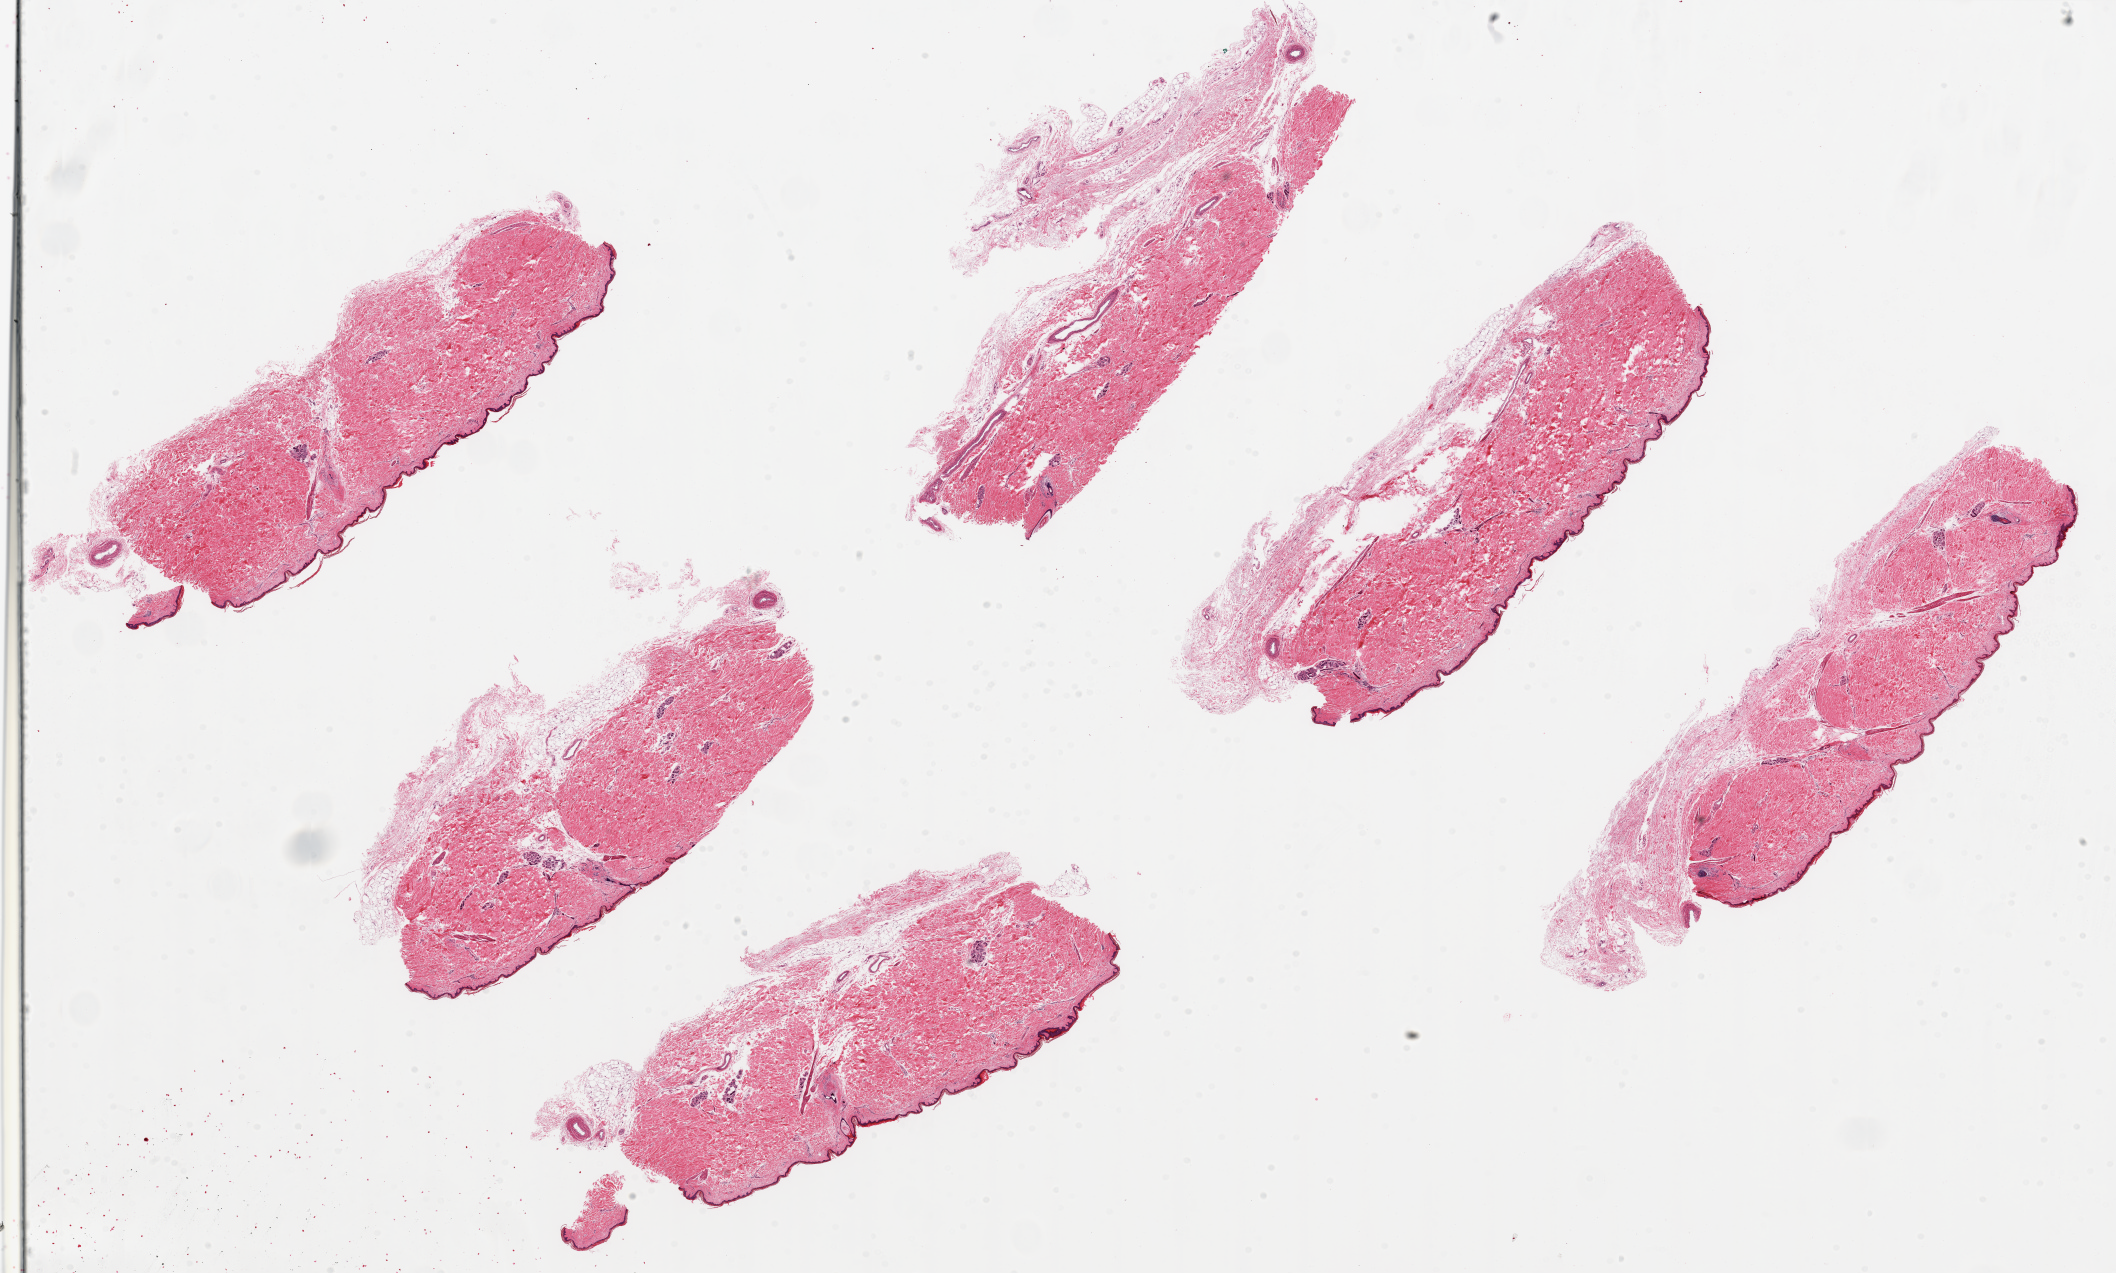
Hematoxylin and eosin (H&E) whole-slide image — whole scanned area (about 33.5 x 20.1 mm) shown as a low-resolution overview; PAXgene-fixed, paraffin-embedded tissue; section of skin of lower leg (target tissue); tissue donor sample.
Reviewer comment on this tissue sample: 6 ~ 8.5x2.5mm pieces; squamous mucosa is ~1-2% of specimen thickness.